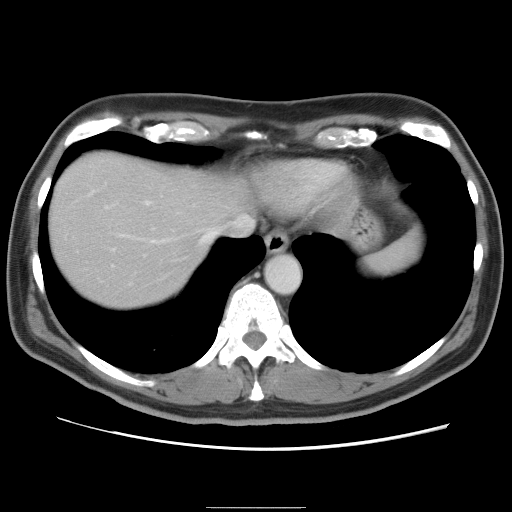
Contrast-enhanced abdominal CT, one axial slice. Slice 72 of 87 in the series (ordered by position). Intravenous contrast given. Soft-tissue window (W 400 / L 40 HU). 5 mm slice thickness. 512 × 512 image matrix, field of view 363 × 363 mm. Male patient, age 63 years. From the clinical record (not read from this slice): diagnosis: colorectal cancer liver metastases, imaged before liver resection; multiple liver metastases: no; largest metastasis: 9 cm; disease in both lobes: no.
Outlined on this slice (outlined manually by an expert reader):
- hepatic veins: bounding box [x1, y1, x2, y2] px = [96, 182, 253, 246]
- liver: [48, 151, 242, 310]
- planned liver remnant (the part of the liver to remain after resection): [49, 170, 206, 309]
- portal vein (with intrahepatic branches): [103, 200, 157, 286]